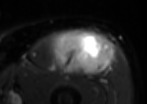
MRI of an extremity soft-tissue mass, one axial slice; slice 45 of 85 in the series (ordered by position); T2-weighted fat-saturated; MR volume resampled by the dataset authors to the PET/CT grid (not the native acquisition matrix); 147 × 104 image matrix, field of view 144 × 102 mm. Male patient. From the clinical record (not read from this slice): histological type: extraskeletal osteosarcoma; grade: high; site of the primary tumour: thigh.
Outlined on this slice (expert contour drawn on MRI and transferred to this co-registered scan by the dataset authors):
- gross tumour volume (mass): box from (x=53, y=30) to (x=111, y=75) px